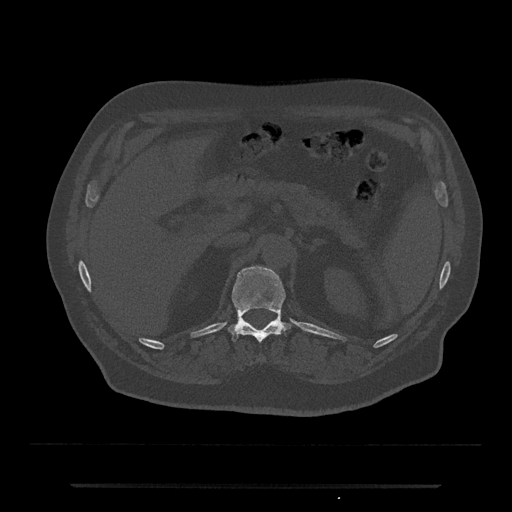
CT including the spine, one axial slice; slice 591 of 797 in the series (ordered by position); reconstruction kernel Br40s/3; 120 kVp; bone window (W 1800 / L 400 HU); 0.5 mm slice thickness; 512 × 512 image matrix. Male patient, age 80 years. Case-level facts recorded for this patient, not image findings: primary cancer: prostate; vertebrae with lytic lesions (as recorded): L1, T11.
Outlined on this slice (semi-automatically segmented with operator editing):
- T12 vertebra: bounding box (x1, y1, x2, y2) in pixels: (228, 266, 291, 343)